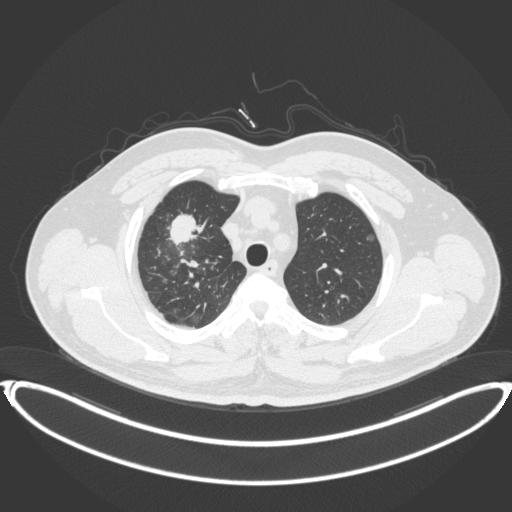
Chest CT, one axial slice. Slice 311 of 399 in the series (ordered by position). Reconstruction kernel B31f. 120 kVp. Lung window (W 1500 / L -600 HU). 1 mm slice thickness. 512 × 512 image matrix, field of view 445 × 445 mm. Patient: male, 53 years. From the clinical record (not read from this slice): clinical TNM (as recorded): T2a N0 M0.
Outlined on this slice (rectangle marked by the reading radiologist):
- lung tumour (recorded histology: adenocarcinoma): bounding box [x1, y1, x2, y2] px = [165, 210, 212, 248]